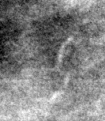
Crop from a digitized film mammogram around one marked abnormality, right breast, MLO view.
- Calcifications, morphology pleomorphic / fine linear branching, distribution segmental; BI-RADS assessment category 5; subtlety rating 5 on a 1 (subtle) to 5 (obvious) scale; pathology result (as recorded, not read from the image): malignant.